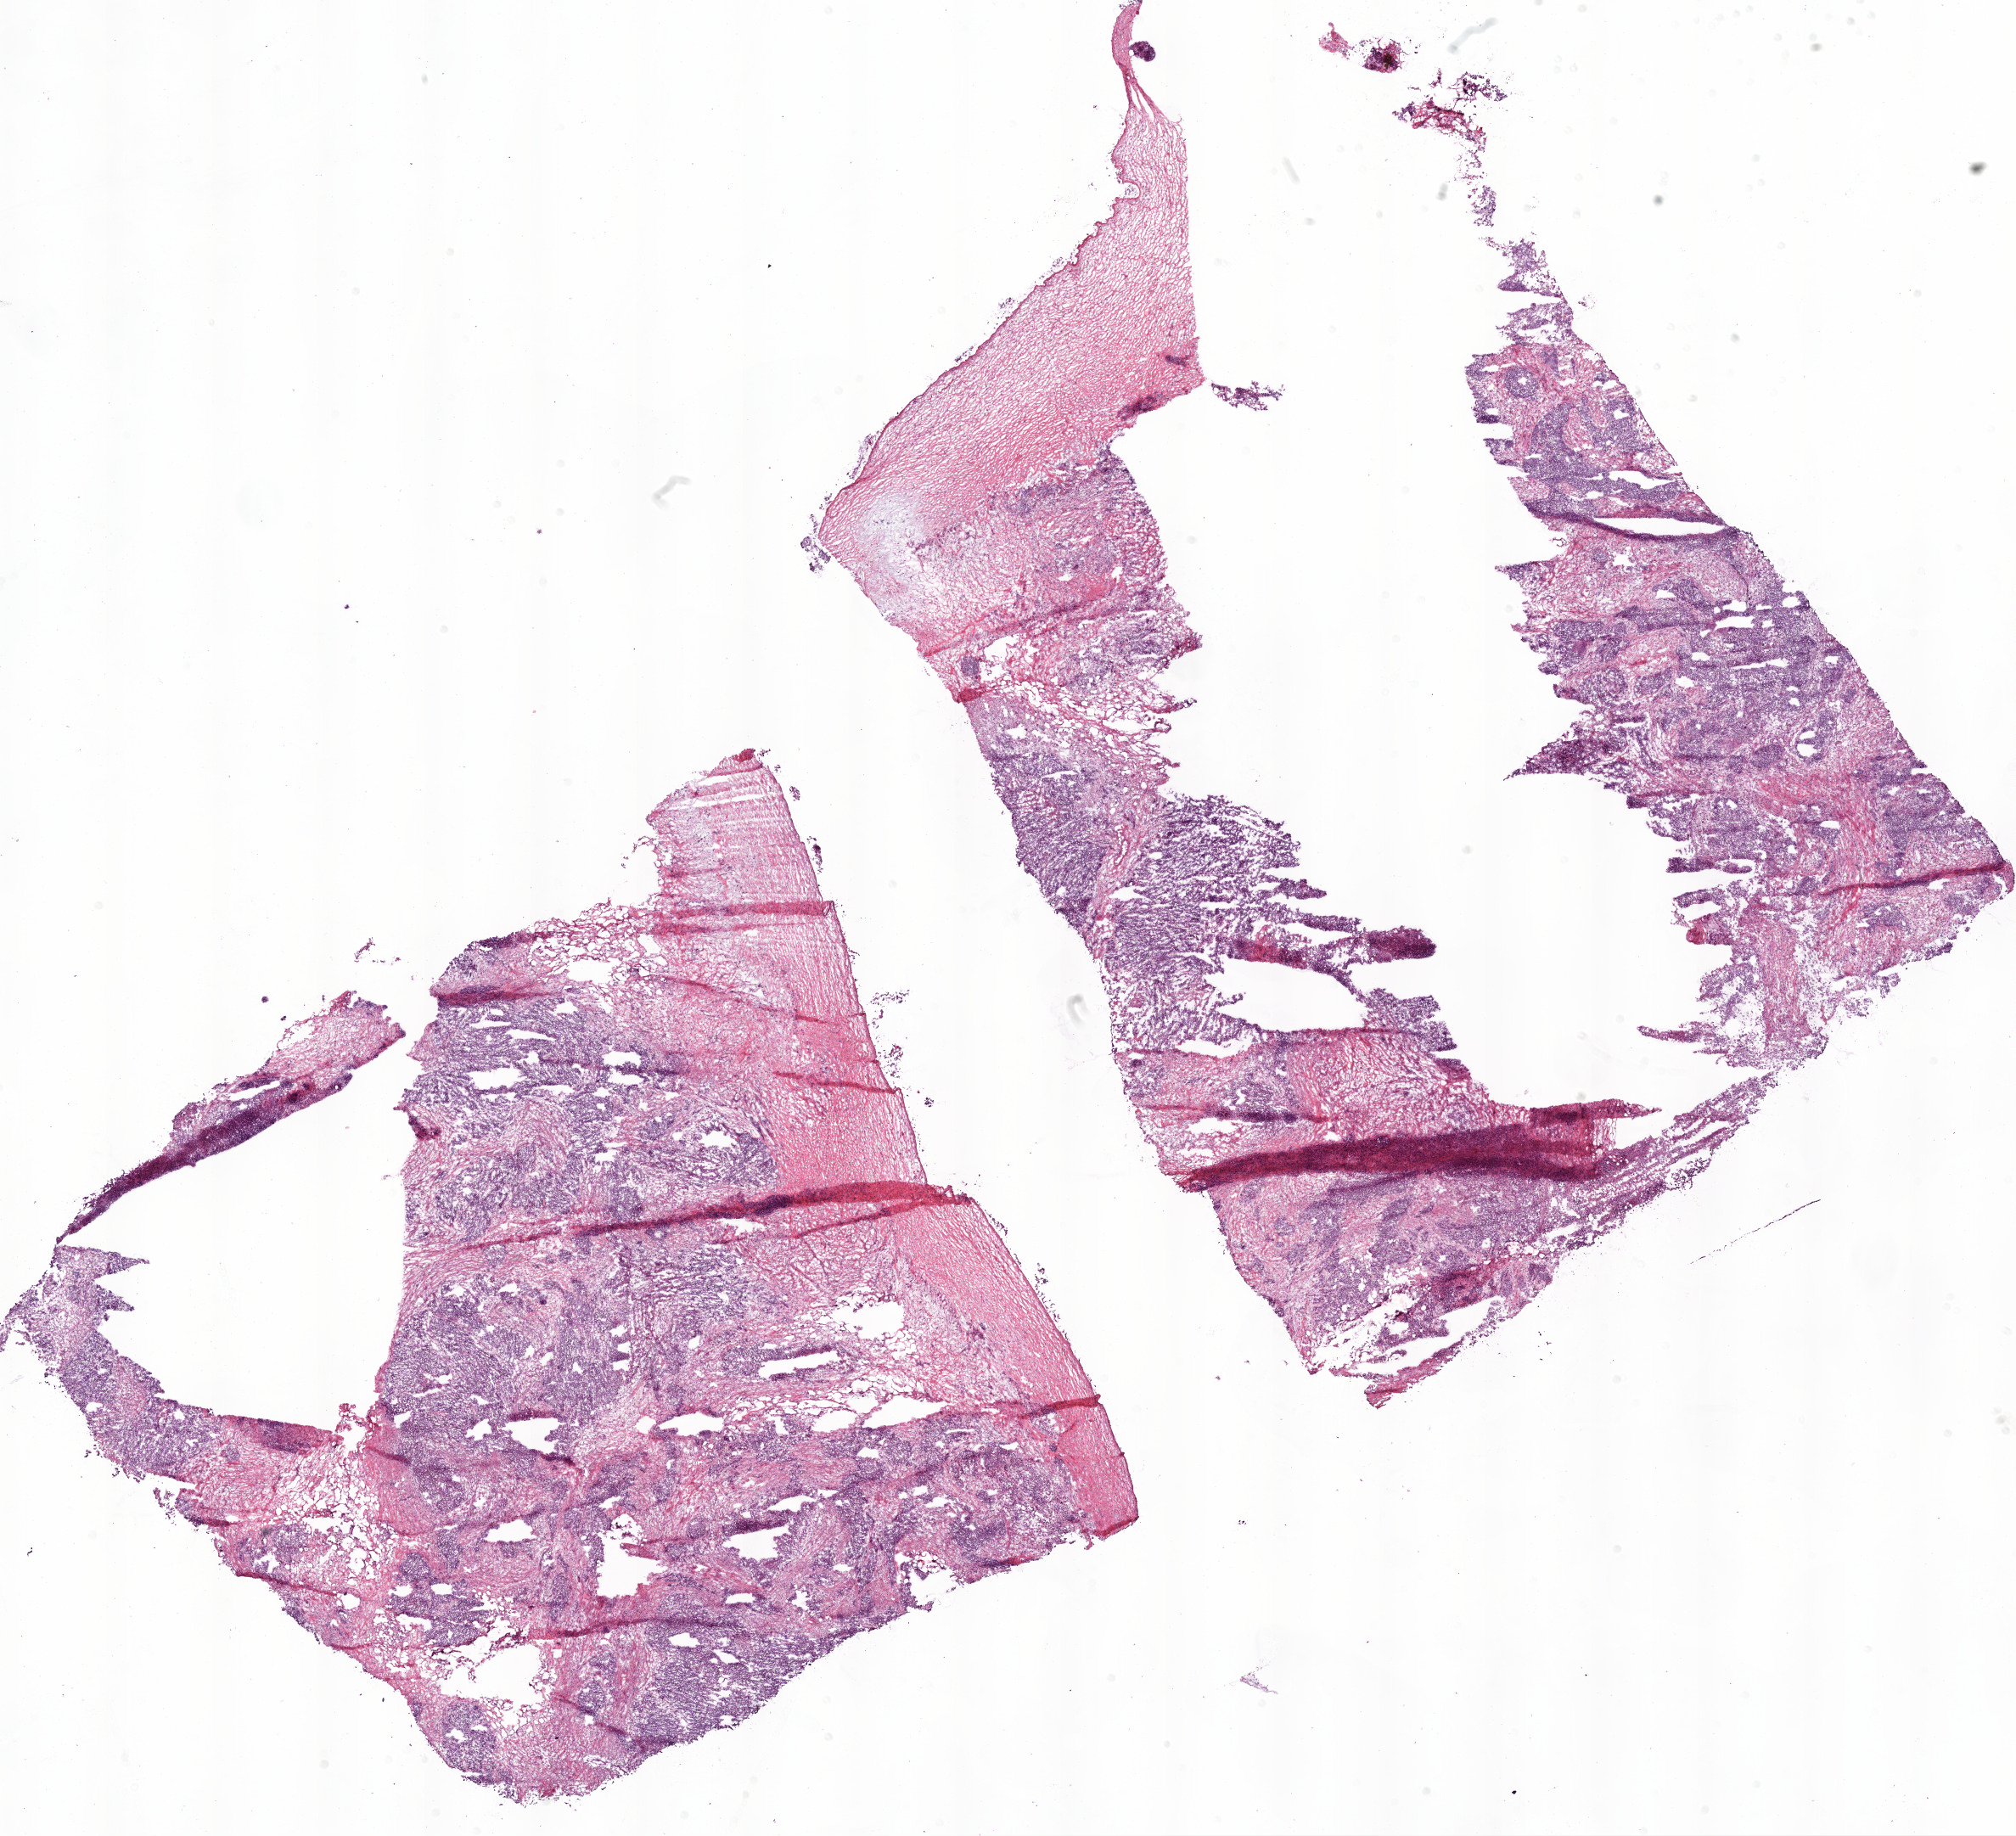
H&E whole-slide image, low-resolution overview of the scanned area, about 19.1 x 17.4 mm. Frozen section from the bottom of the tissue portion. Ovary, primary tumour sample. Female patient; age at initial diagnosis 61 years. Histologic grade: G3 (poorly differentiated). Slide review estimates, as recorded: tumour cells 50%, tumour nuclei 75%, normal cells 0%, stromal cells 45%, necrosis 5%. Infiltration values recorded for this section: lymphocyte infiltration 40%, monocyte infiltration 10%, neutrophil infiltration 50%.
- diagnosis: Serous cystadenocarcinoma, NOS
- FIGO stage: IIIC